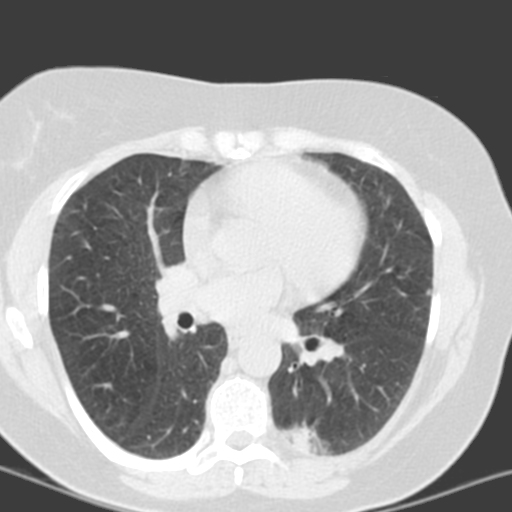
Low-dose screening chest CT, axial slice. Third screening round (two years after baseline). Lung window (W 1500 / L -600 HU). 3.2 mm slice thickness. Standard (soft-tissue) reconstruction kernel (B). Slice 68 of 150 in the series. Female, age 55 years at enrolment. Current smoker at enrolment.
Expert-annotated lung lesion, bounding box <280,406,360,461> (left, top, right, bottom; pixels). The screening reader recorded 6 non-calcified nodules or masses ≥4 mm on this exam (left lower lobe, left lower lobe, left upper lobe, lingula, lingula, right middle lobe); which of them this box marks is not recorded. Later outcome: lung cancer diagnosed 357 days after this screen — adenocarcinoma with mixed subtypes, left lower lobe, poorly differentiated (G3), stage IA (AJCC 6th edition), 21 mm at pathology.